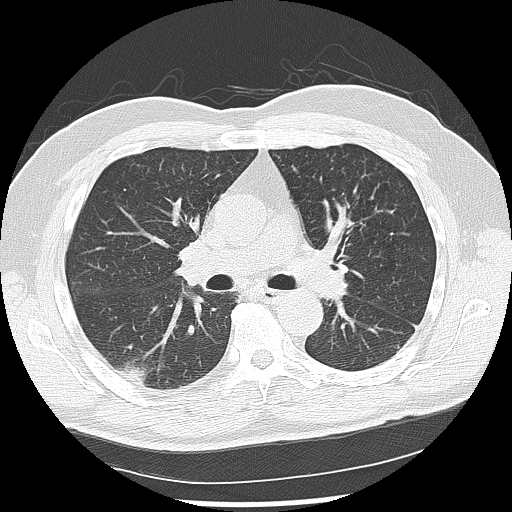
Low-dose screening chest CT, one axial slice. Slice 79 of 142 in the series (ordered by position). Reconstruction kernel LUNG. Lung window (W 1500 / L -600 HU). 512 × 512 image matrix.
Outlined on this slice (outlined manually by an expert reader):
- lesion 2 (nodule, lower lobe of right lung): box from (x=121, y=362) to (x=148, y=385) px